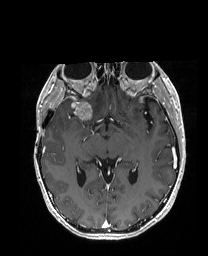
Brain MRI from a brain-tumour surgery series, one axial slice. Position 102 of 192 along the scan axis. T1-weighted post-contrast. 1 mm slice thickness. 208 × 256 image matrix, field of view 203 × 250 mm. Case-level facts recorded for this patient, not image findings: histopathology: Metastatic Carcinoma from Breast primary; tumour location: Right Frontal.
Annotated regions visible in this slice (outlined manually by an expert reader):
- tumour: box from (x=55, y=98) to (x=104, y=119) px